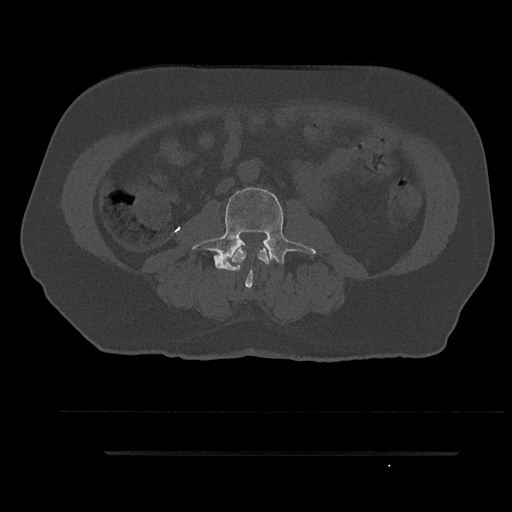
CT including the spine, one axial slice. Slice 55 of 797 in the series (ordered by position). Reconstruction kernel Br40s/3. 120 kVp. Bone window (W 1800 / L 400 HU). 0.5 mm slice thickness. 512 × 512 image matrix, field of view 432 × 432 mm. Male patient, age 63 years. Case-level facts recorded for this patient, not image findings: primary cancer: renal; vertebrae with lytic lesions (as recorded): T8.
Structures marked on this image (semi-automatic segmentation, software-assisted and operator-edited):
- L2 vertebra: box from (x=232, y=248) to (x=270, y=271) px
- L3 vertebra: (x=192, y=185)–(x=316, y=288)